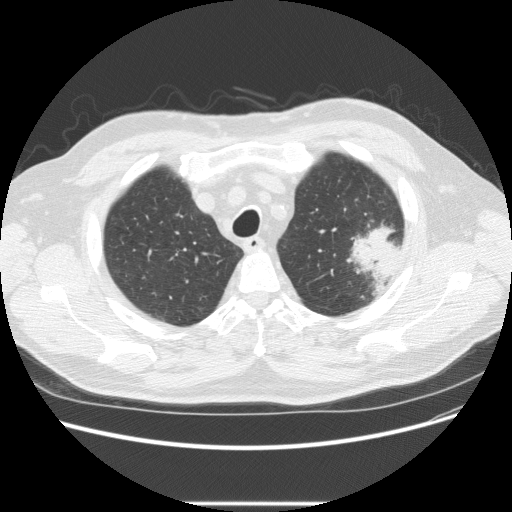
Chest CT (low-dose screening protocol), one axial image, baseline annual screen, lung window (W 1500 / L -600 HU), 2.5 mm slice thickness, standard (soft-tissue) reconstruction kernel (STANDARD), slice 47 of 233 in the series. Male, age 73 years at enrolment. Former smoker at enrolment.
- Expert-annotated lung lesion, bounding box (x1, y1, x2, y2) in pixels: (332, 216, 410, 284).
- The screening reader recorded 2 non-calcified nodules or masses ≥4 mm on this exam (left upper lobe, right upper lobe); which of them this box marks is not recorded.
- Official screen result: positive, change unspecified: nodule(s) >= 4 mm or enlarging nodule(s), mass(es), or other non-specific abnormalities suspicious for lung cancer.
- Lung cancer was diagnosed 11 days after this screen: bronchiolo-alveolar adenocarcinoma, NOS, other location, well differentiated (G1), stage IV (AJCC 6th edition).